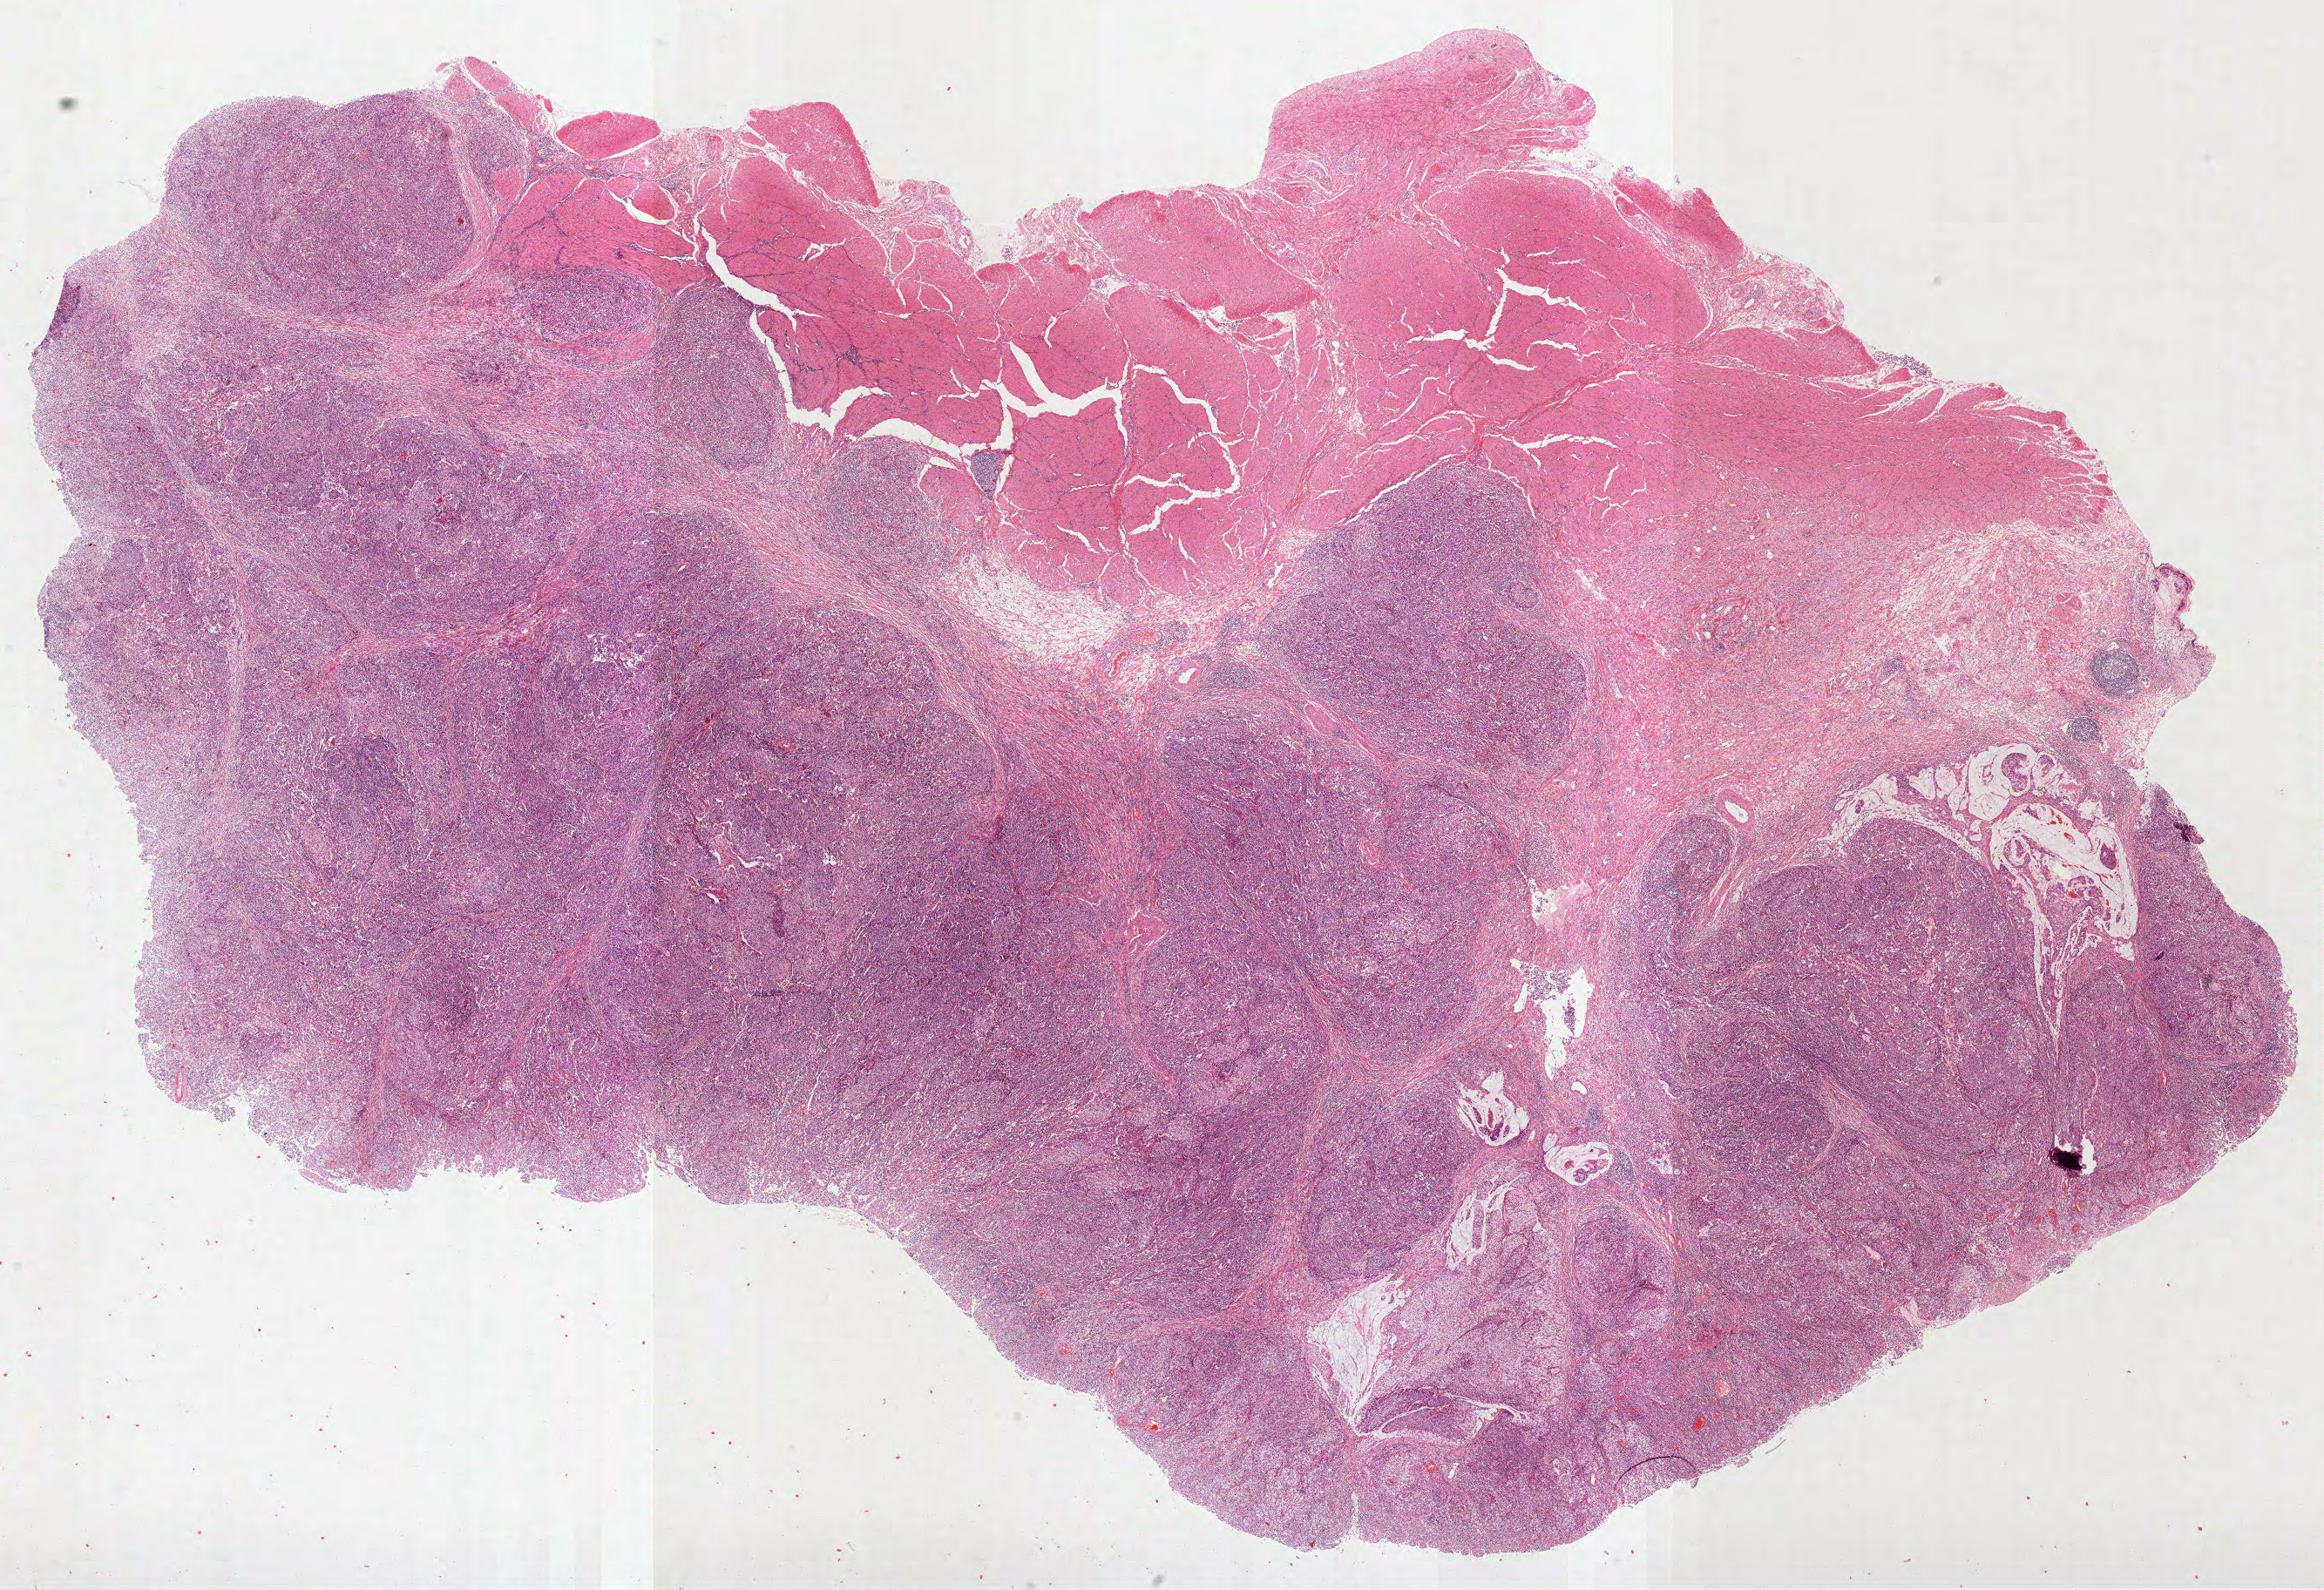
Hematoxylin and eosin (H&E) stained whole-slide image — low-resolution overview of the scanned area, about 21.5 x 14.7 mm, formalin-fixed paraffin-embedded (FFPE) diagnostic section, stomach, primary tumour sample. Patient: female, age at initial diagnosis 84 years. Histologic grade: G3 (poorly differentiated).
Pathologic diagnosis: Adenocarcinoma, NOS (fundus of stomach). AJCC pathologic stage: IB (7th edition). Lymph nodes positive (case pathology): 0 of 15 examined.